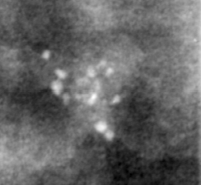
Region of interest cut from a scanned film mammogram (one marked finding), left breast, CC view.
Finding: calcifications, morphology pleomorphic, distribution clustered; BI-RADS assessment category 4; pathology result (as recorded, not read from the image): malignant.